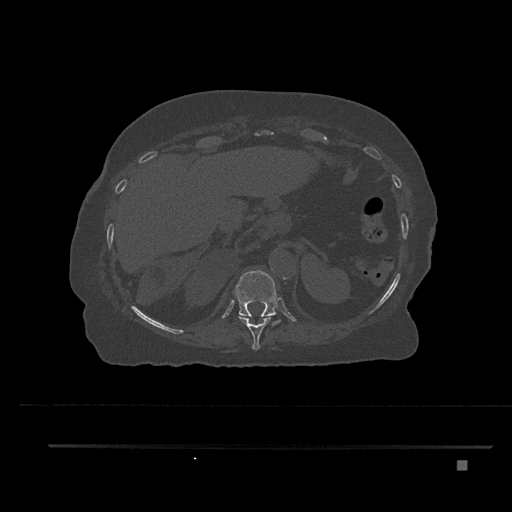
CT including the spine, one axial slice. Position 330 of 797 along the scan axis. Reconstruction kernel Br40s/3. 120 kVp. Bone window (W 1800 / L 400 HU). 0.5 mm slice thickness. 512 × 512 image matrix. Female patient, age 76 years. From the clinical record (not read from this slice): primary cancer: lung; vertebrae with lytic lesions (as recorded): T11, L3.
Structures marked on this image (semi-automatically segmented with operator editing):
- T10 vertebra: bounding box <238,316,271,350> (left, top, right, bottom; pixels)
- T11 vertebra: <234,270,281,326>